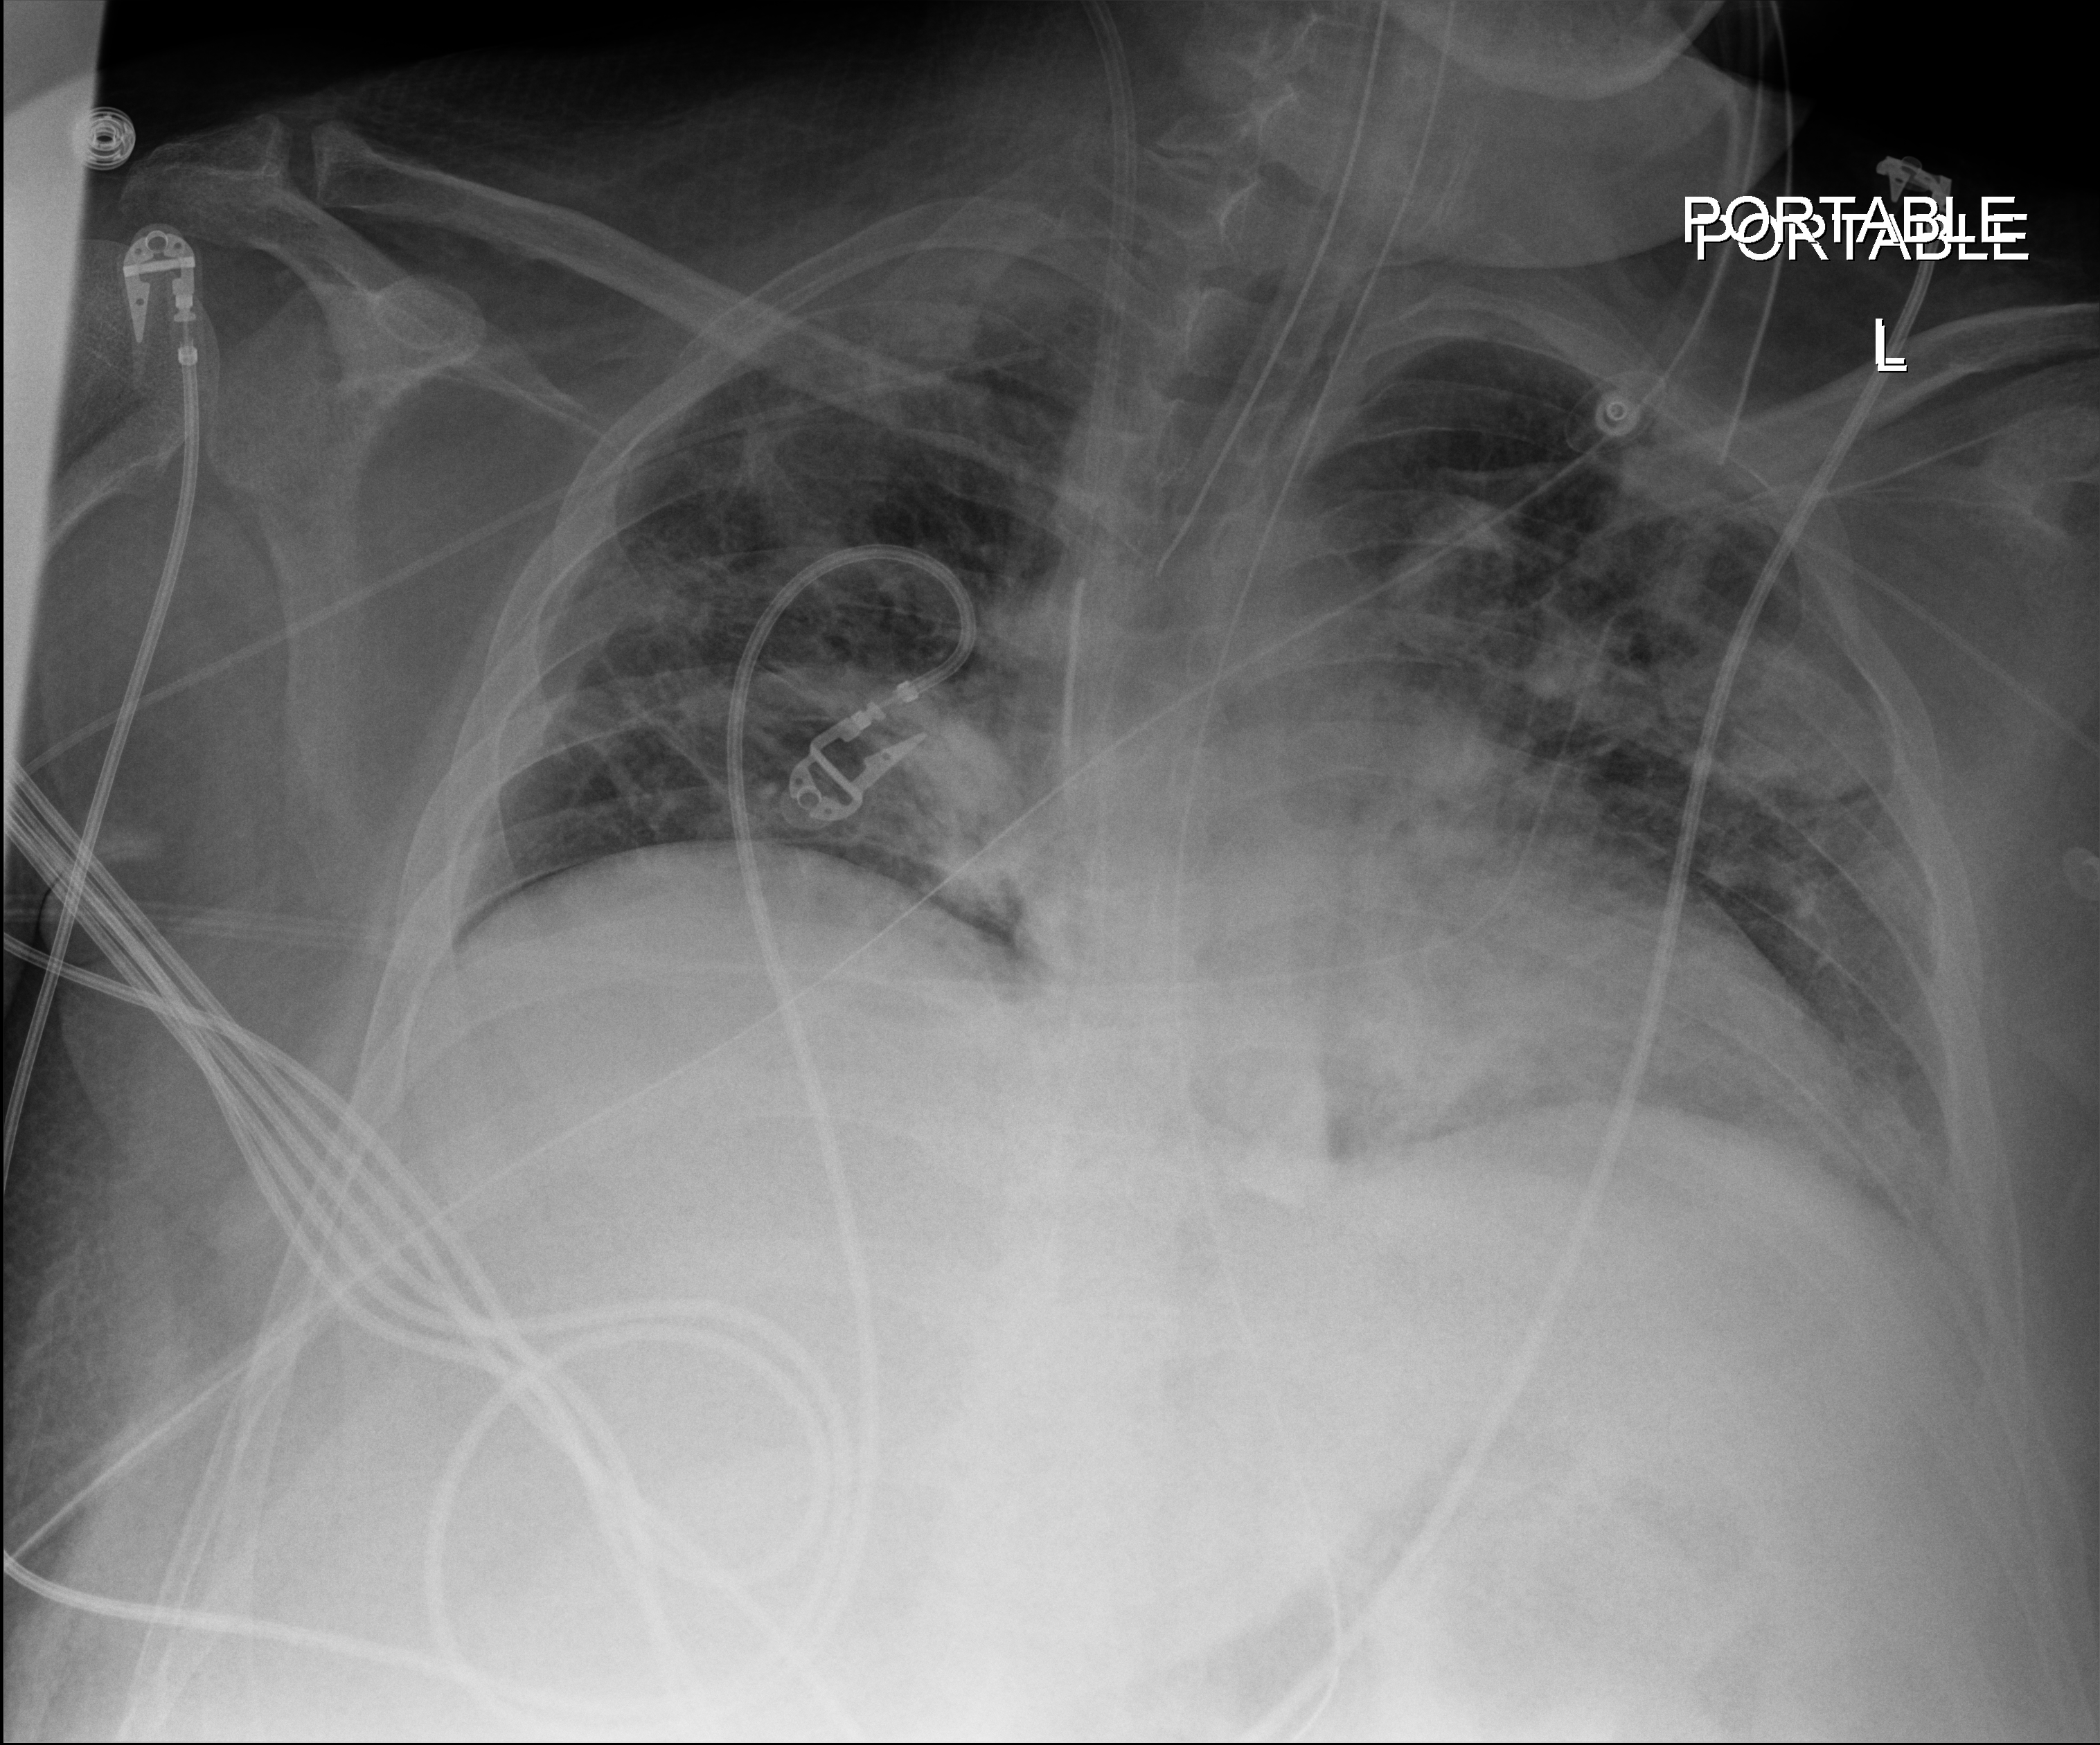
Chest radiograph. Patient hospitalised with COVID-19, aged 18–59 years.
From the hospital-stay record, not from the radiograph (when in the stay this image was taken is not recorded): admitted to intensive care during this hospital stay: yes; diabetes (admission record): no.